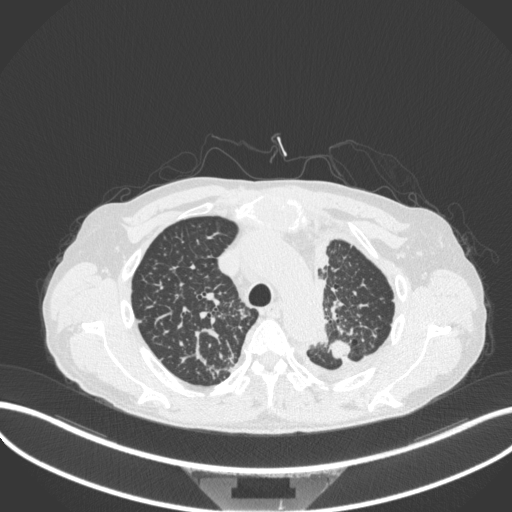
Chest CT, one axial slice. Position 271 of 319 along the scan axis. Reconstruction kernel B31f. 120 kVp. Lung window (W 1500 / L -600 HU). 1 mm slice thickness. 512 × 512 image matrix. Patient: male, 58 years. Case-level facts recorded for this patient, not image findings: clinical TNM (as recorded): T1c N3 M1.
Structures marked on this image (bounding box drawn by a radiologist):
- lung tumour (recorded histology: adenocarcinoma): box from (x=324, y=339) to (x=353, y=361) px